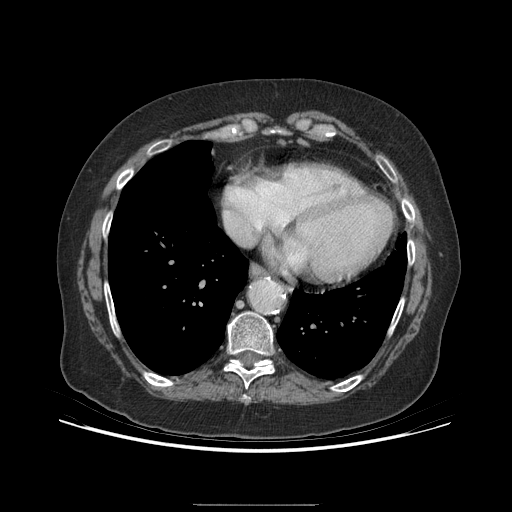
Contrast-enhanced abdominal CT (liver protocol), one axial slice. Position 189 of 192 along the scan axis. Reconstruction kernel STANDARD. 140 kVp. Soft-tissue window (W 400 / L 40 HU). 2.5 mm slice thickness. 512 × 512 image matrix, field of view 400 × 400 mm. From the clinical record (not read from this slice): diagnosis: hepatocellular carcinoma (patient treated with transarterial chemoembolisation; whether this scan precedes or follows treatment is not stated here); TNM stage (as recorded): Stage-I; Child-Pugh class: A; tumour nodularity: uninodular; tumour size: 3.2 cm.
Structures marked on this image (semi-automatically segmented with operator editing):
- abdominal aorta: bounding box (x1, y1, x2, y2) in pixels: (250, 281, 280, 311)